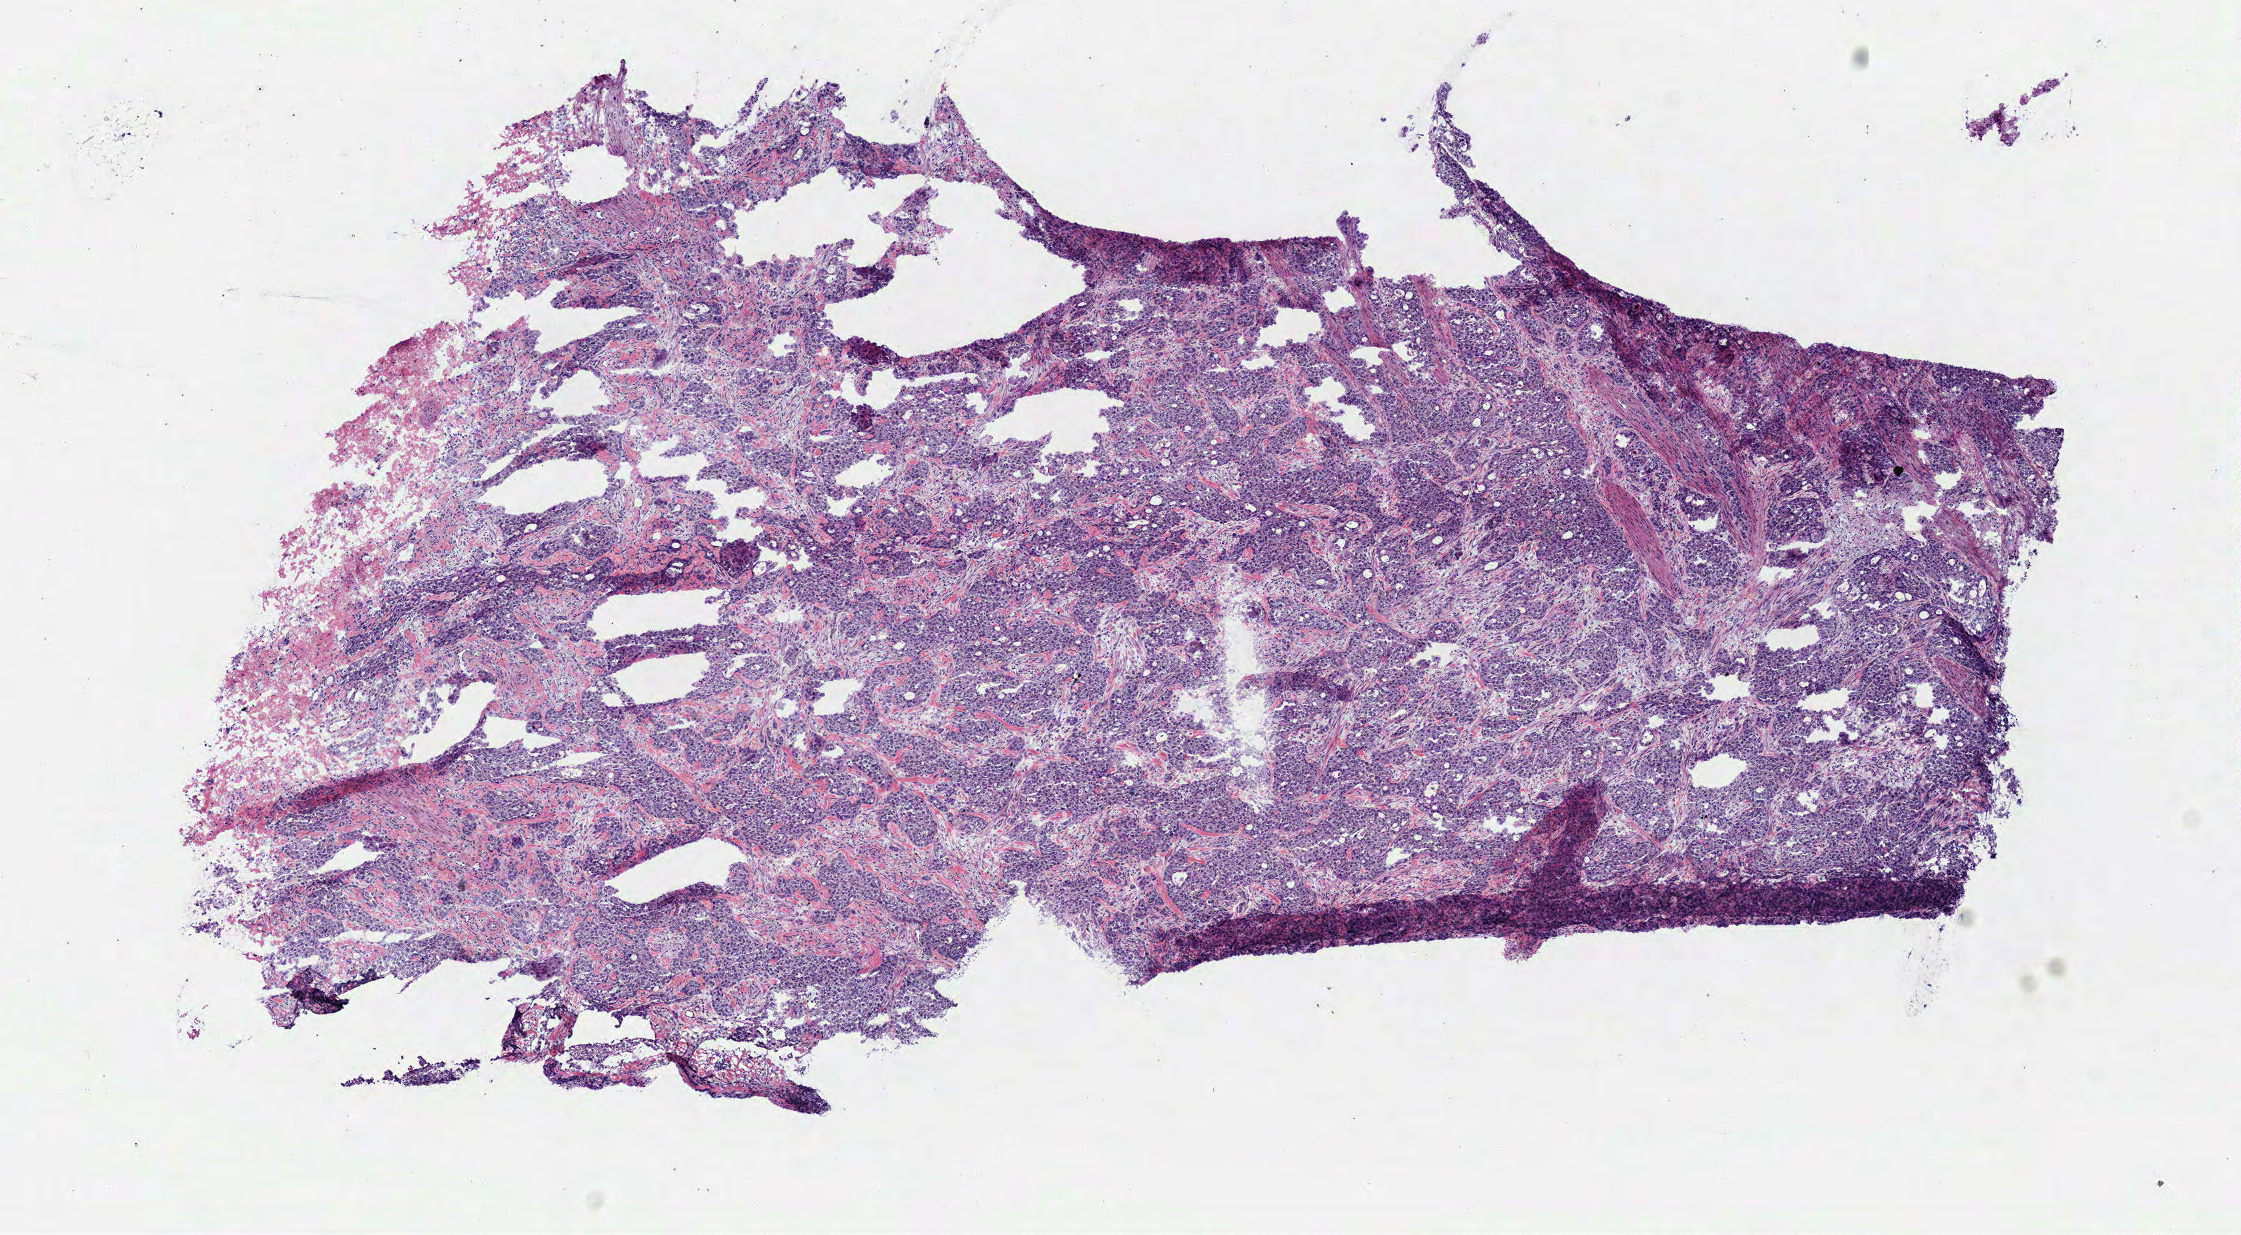
Whole-slide histology image, H&E-stained, shown as a low-resolution overview of the whole scanned area (about 8.8 x 4.9 mm, acquisition: 40x scan), frozen section from the bottom of the tissue portion, sample: primary tumour, stomach. Patient: female, age at initial diagnosis 64 years. Histologic grade: G3 (poorly differentiated). Pathologist review of this section (percent, as recorded): tumour cells 85%, tumour nuclei 85%, normal cells 0%, stromal cells 15%, necrosis 0%.
Pathologic diagnosis: Carcinoma, diffuse type (cardia, NOS). Lymph nodes positive (case pathology): 2 of 16 examined.